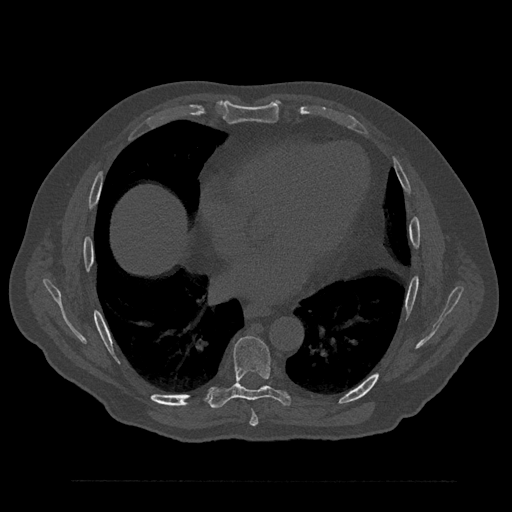
CT including the spine, one axial slice. Slice 459 of 797 in the series (ordered by position). Reconstruction kernel Br40s/3. 120 kVp. Bone window (W 1800 / L 400 HU). 0.5 mm slice thickness. 512 × 512 image matrix, field of view 430 × 430 mm. Patient: male, 61 years. From the clinical record (not read from this slice): primary cancer: prostate.
Annotated regions visible in this slice (semi-automatic segmentation, software-assisted and operator-edited):
- T7 vertebra: box from (x=250, y=410) to (x=259, y=426) px
- T8 vertebra: (x=208, y=336)–(x=292, y=409)